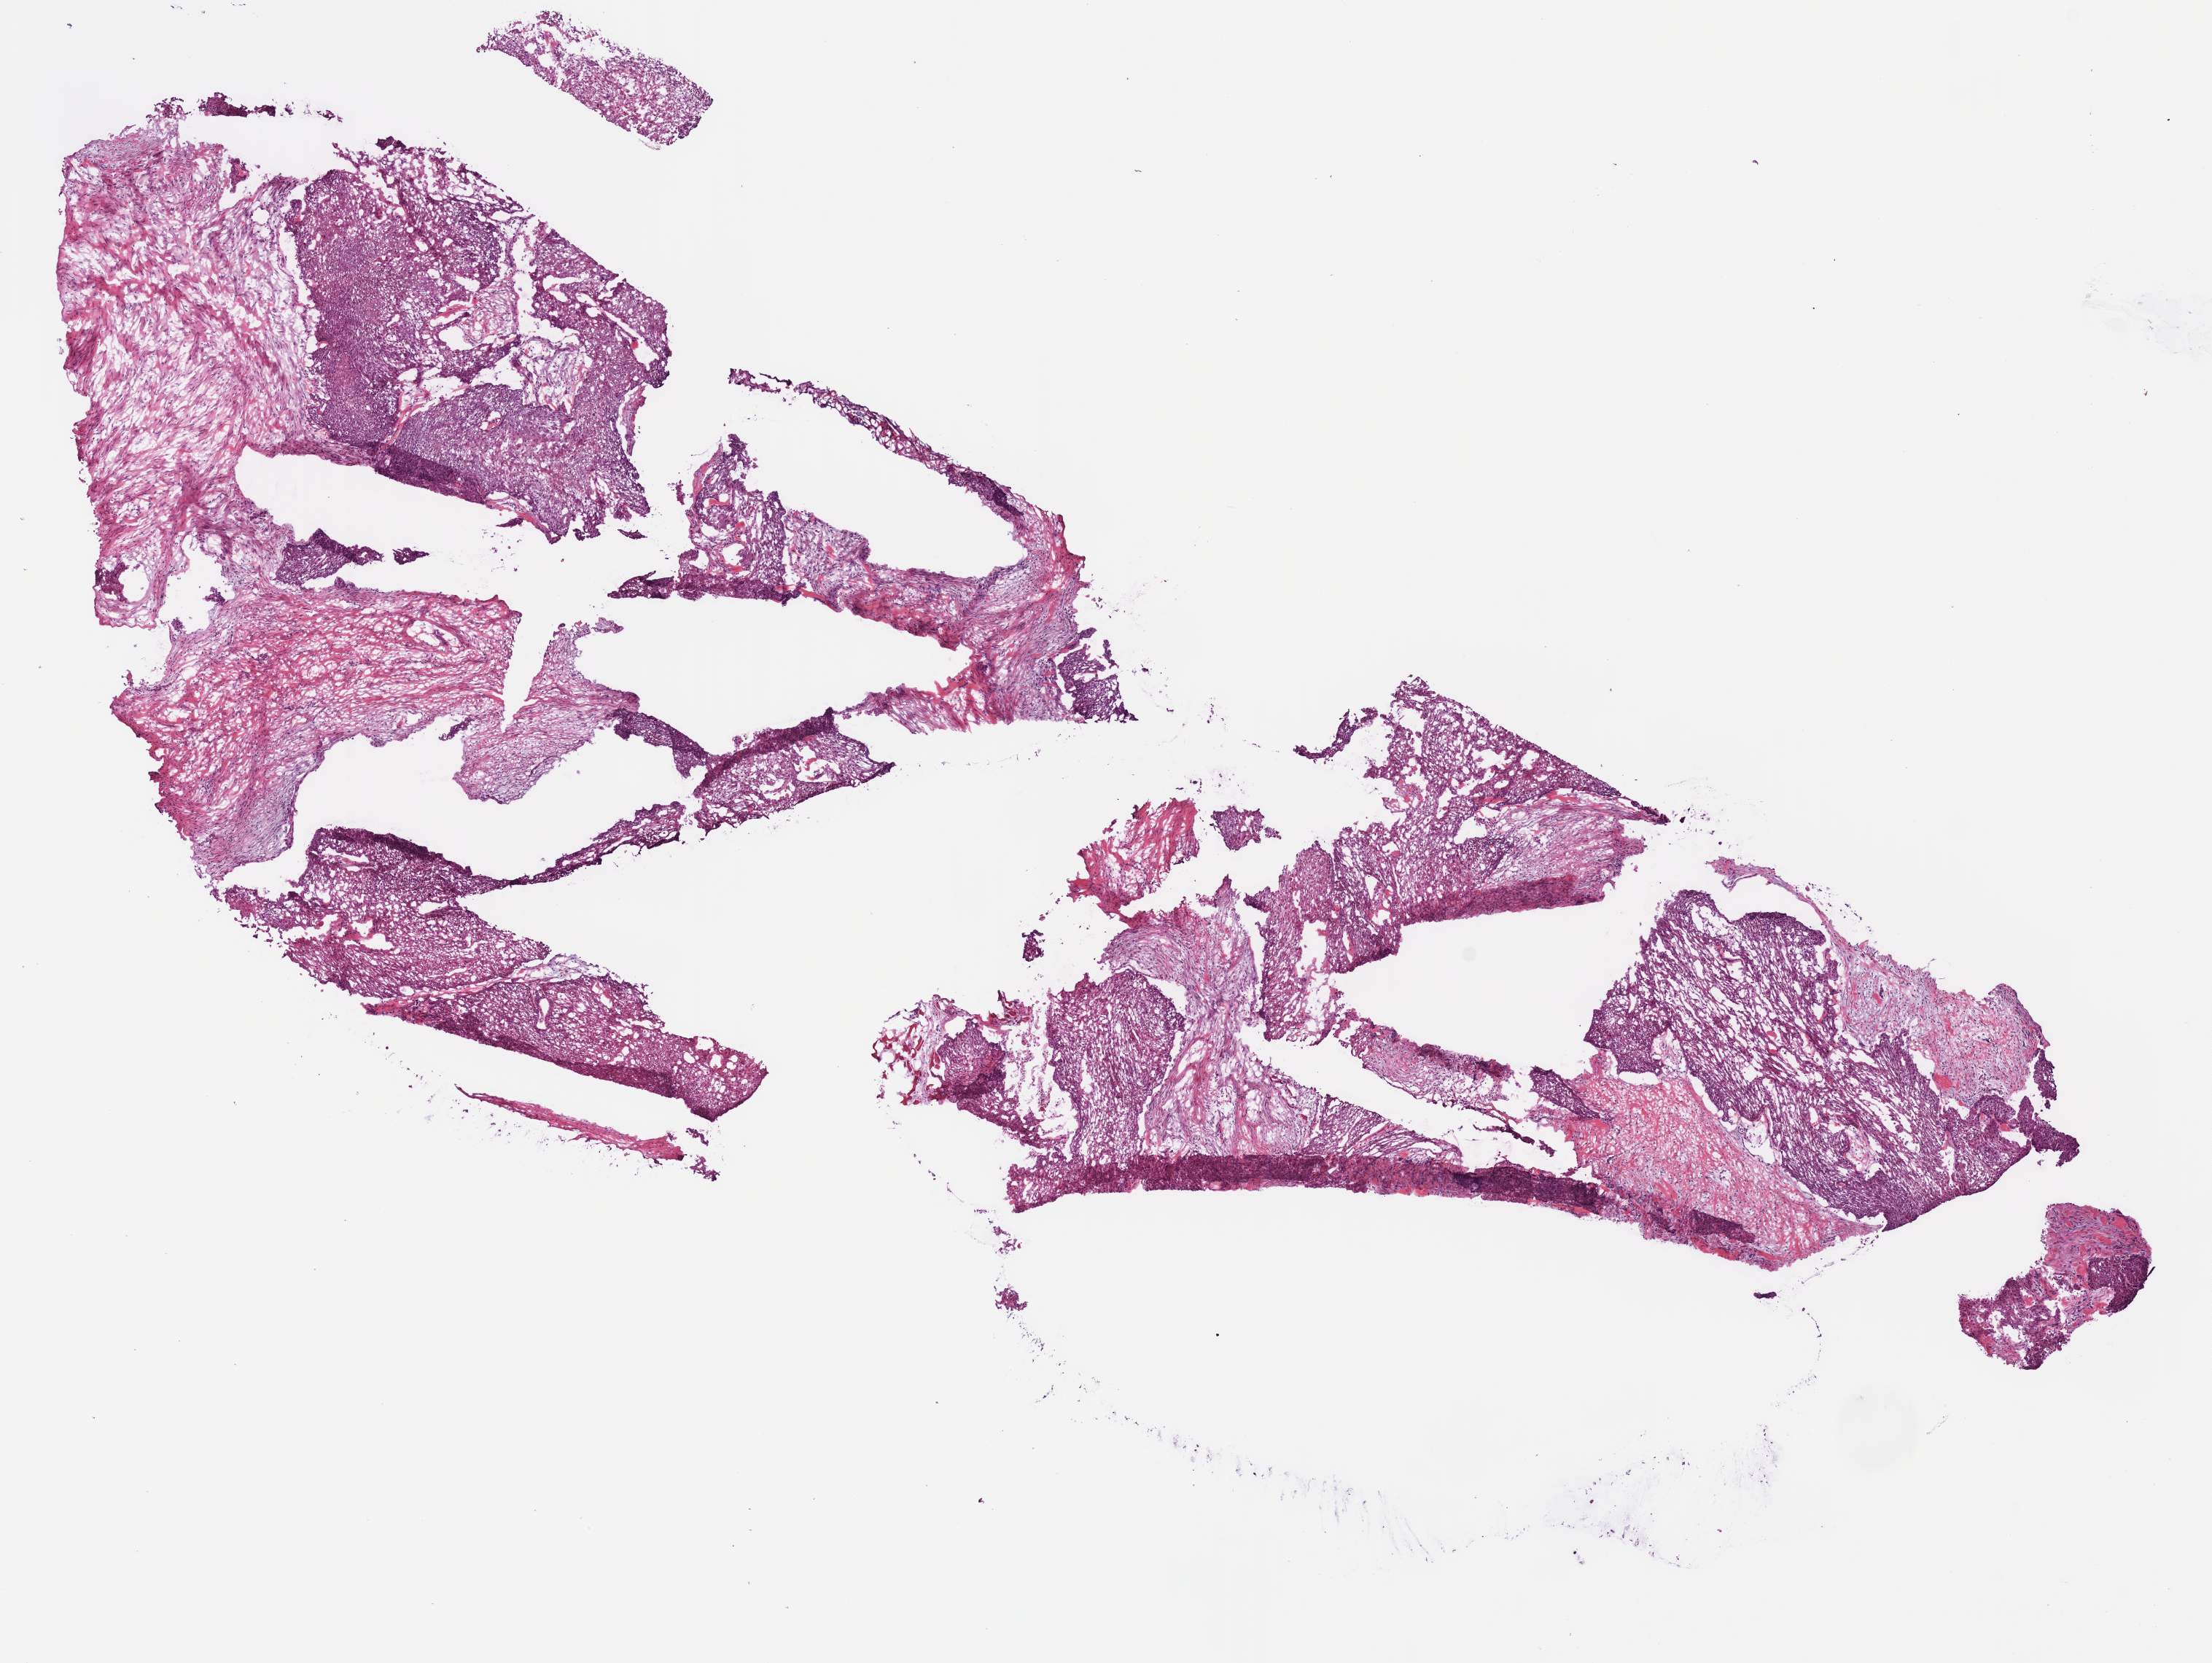
Digitized Hematoxylin and eosin (H&E) stained tissue section (whole slide), a low-resolution overview of the entire scanned area, about 12.0 x 9.0 mm (acquisition: 40x scan). Frozen section from the bottom of the tissue portion. Primary tumour sample from the head and neck. Patient: male, age at initial diagnosis 78 years. Histologic grade: G2 (moderately differentiated). Pathologist review of this section (percent, as recorded): tumour cells 65%, tumour nuclei 71%, normal cells 0%, stromal cells 35%, necrosis 0%. Infiltration values recorded for this section: lymphocyte infiltration 2%, monocyte infiltration 0%, neutrophil infiltration 0%.
- histologic diagnosis: Squamous cell carcinoma, NOS
- AJCC pathologic stage: IVA
- laterality: left